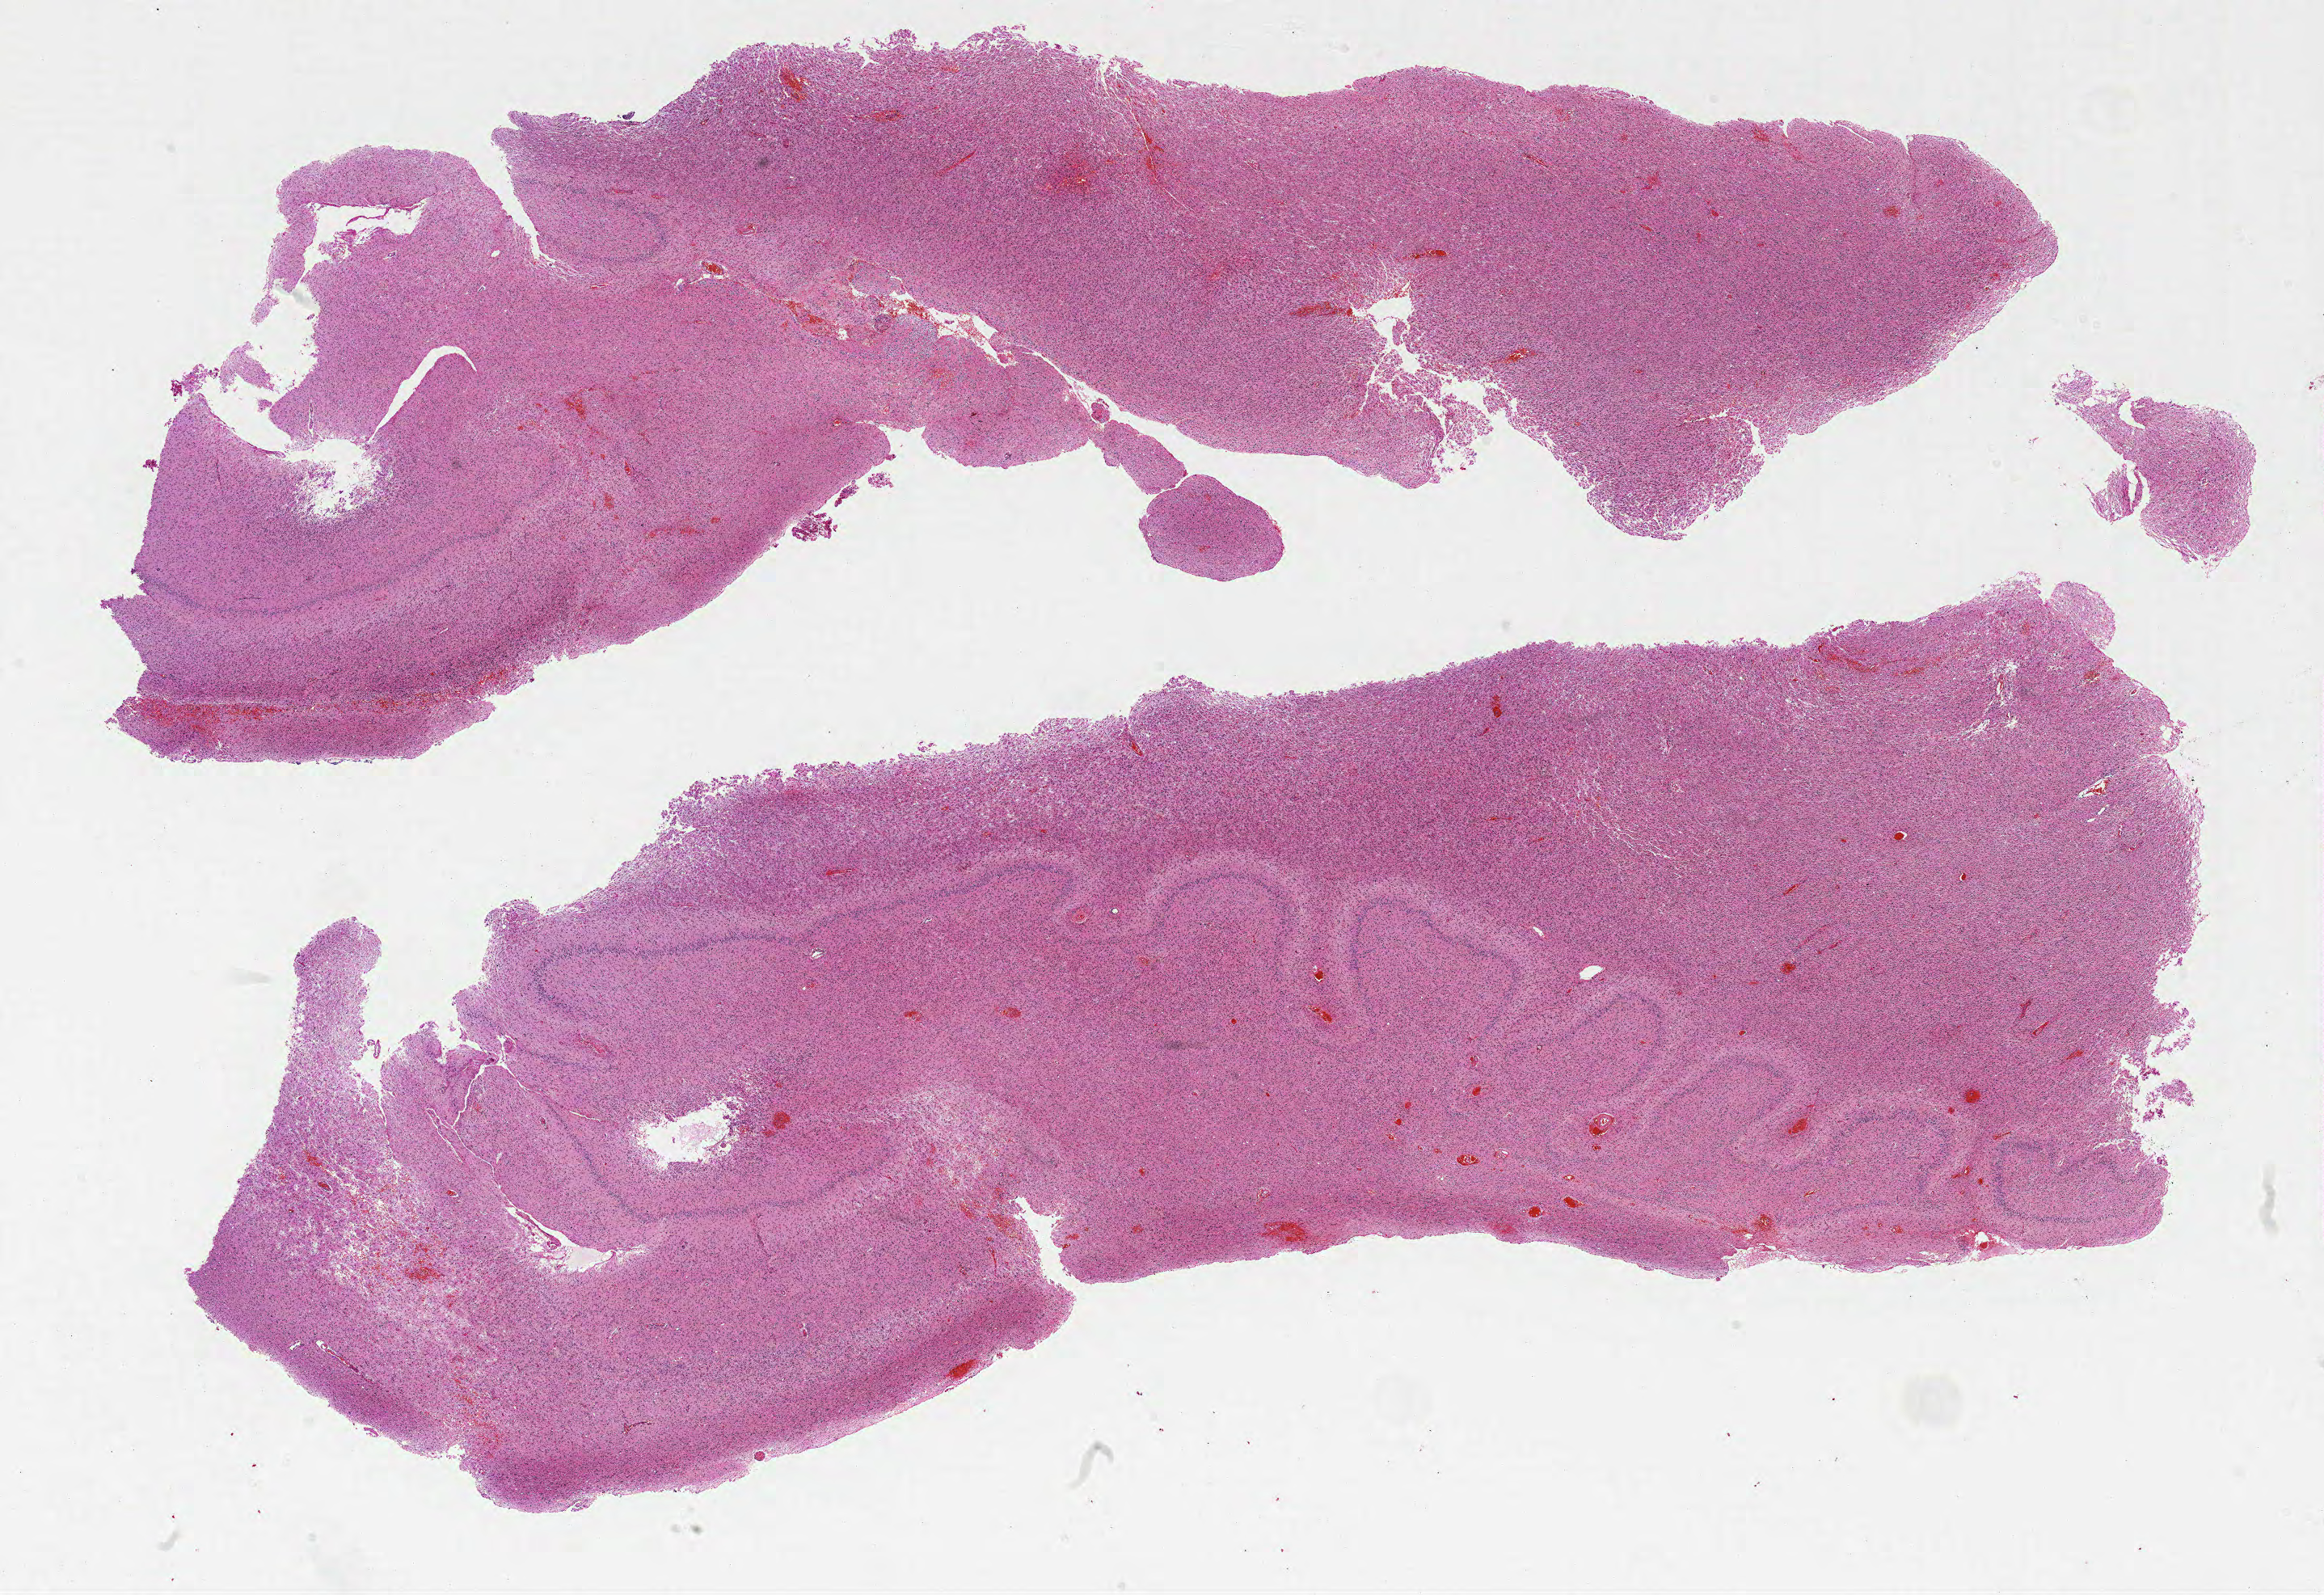
Digitized H&E-stained tissue section (whole slide) — low-resolution overview of the scanned area, about 23.0 x 15.8 mm (slide scanned at 20x), formalin-fixed paraffin-embedded (FFPE) diagnostic section, primary tumour sample from the brain. Female, age 75 years at initial diagnosis.
Diagnosis: Glioblastoma.